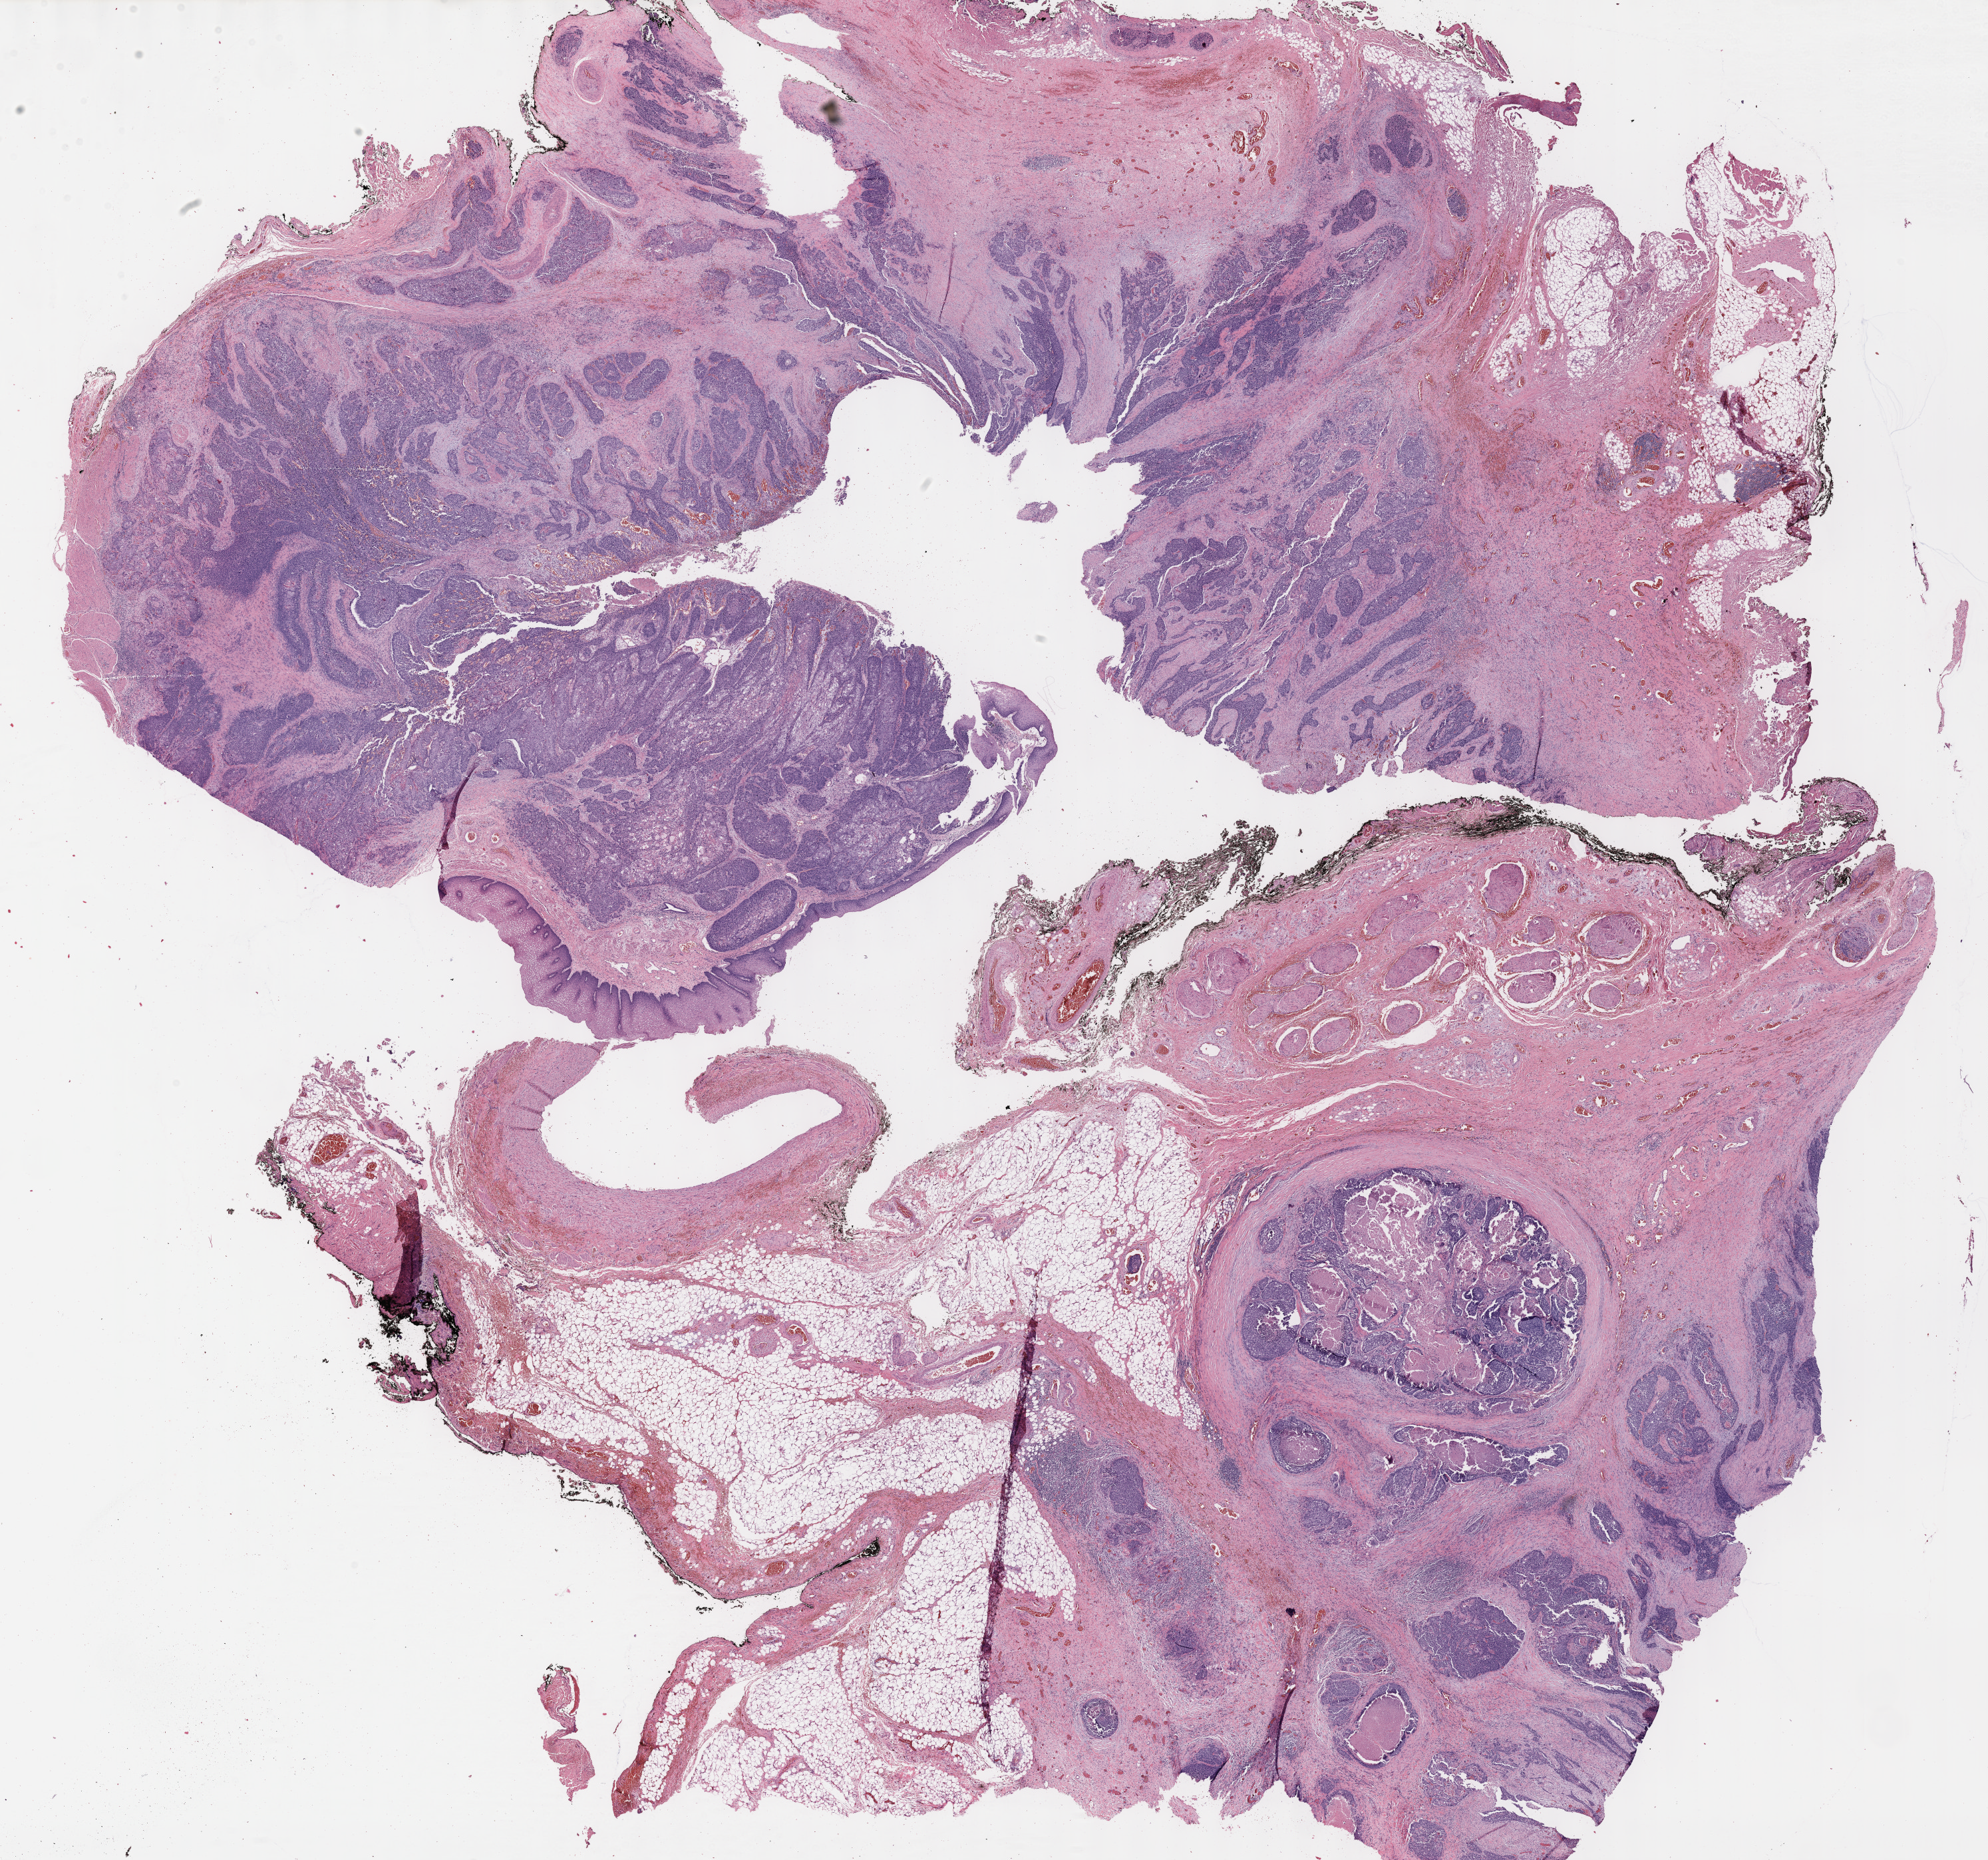
Whole-slide histology image, H&E-stained, low-resolution overview of the scanned area, about 24.1 x 22.6 mm (slide scanned at 40x); formalin-fixed paraffin-embedded (FFPE) diagnostic section; esophagus, primary tumour sample. Male, age 51 years at initial diagnosis. Histologic grade: G3 (poorly differentiated).
Lymph nodes positive (case pathology): 4 of 27 examined. Histologic diagnosis: Squamous cell carcinoma, NOS. AJCC pathologic stage: IIIB.